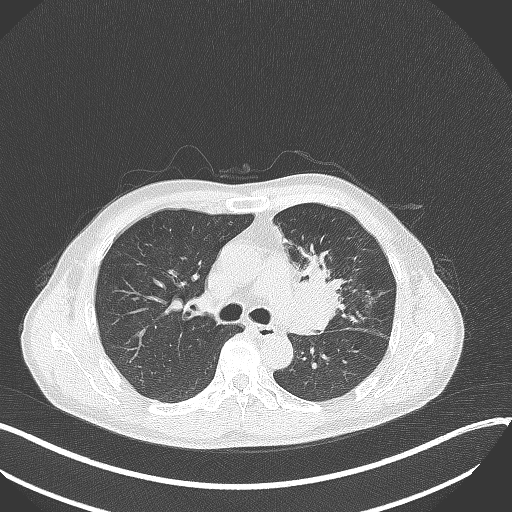
Chest CT, one axial slice. Position 213 of 411 along the scan axis. 120 kVp. Lung window (W 1500 / L -600 HU). 1 mm slice thickness. 512 × 512 image matrix. Patient: male, 56 years. Case-level facts recorded for this patient, not image findings: clinical TNM (as recorded): T2a N0 M0.
Annotated regions visible in this slice (bounding box drawn by a radiologist):
- lung tumour (recorded histology: squamous cell carcinoma): bounding box (x1, y1, x2, y2) in pixels: (288, 250, 344, 331)